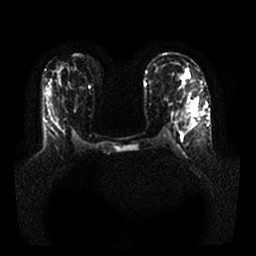
Breast MRI, one axial slice. Position 17 of 25 along the scan axis. Diffusion-weighted series; image 2 of 4 stored at this slice position (different b-values; order by instance number). 1.5 T. 4 mm slice thickness. 256 × 256 image matrix, field of view 340 × 340 mm. Female patient.
Outlined on this slice (manually delineated by an expert):
- tumour on diffusion-weighted imaging: bounding box <191,100,197,116> (left, top, right, bottom; pixels)